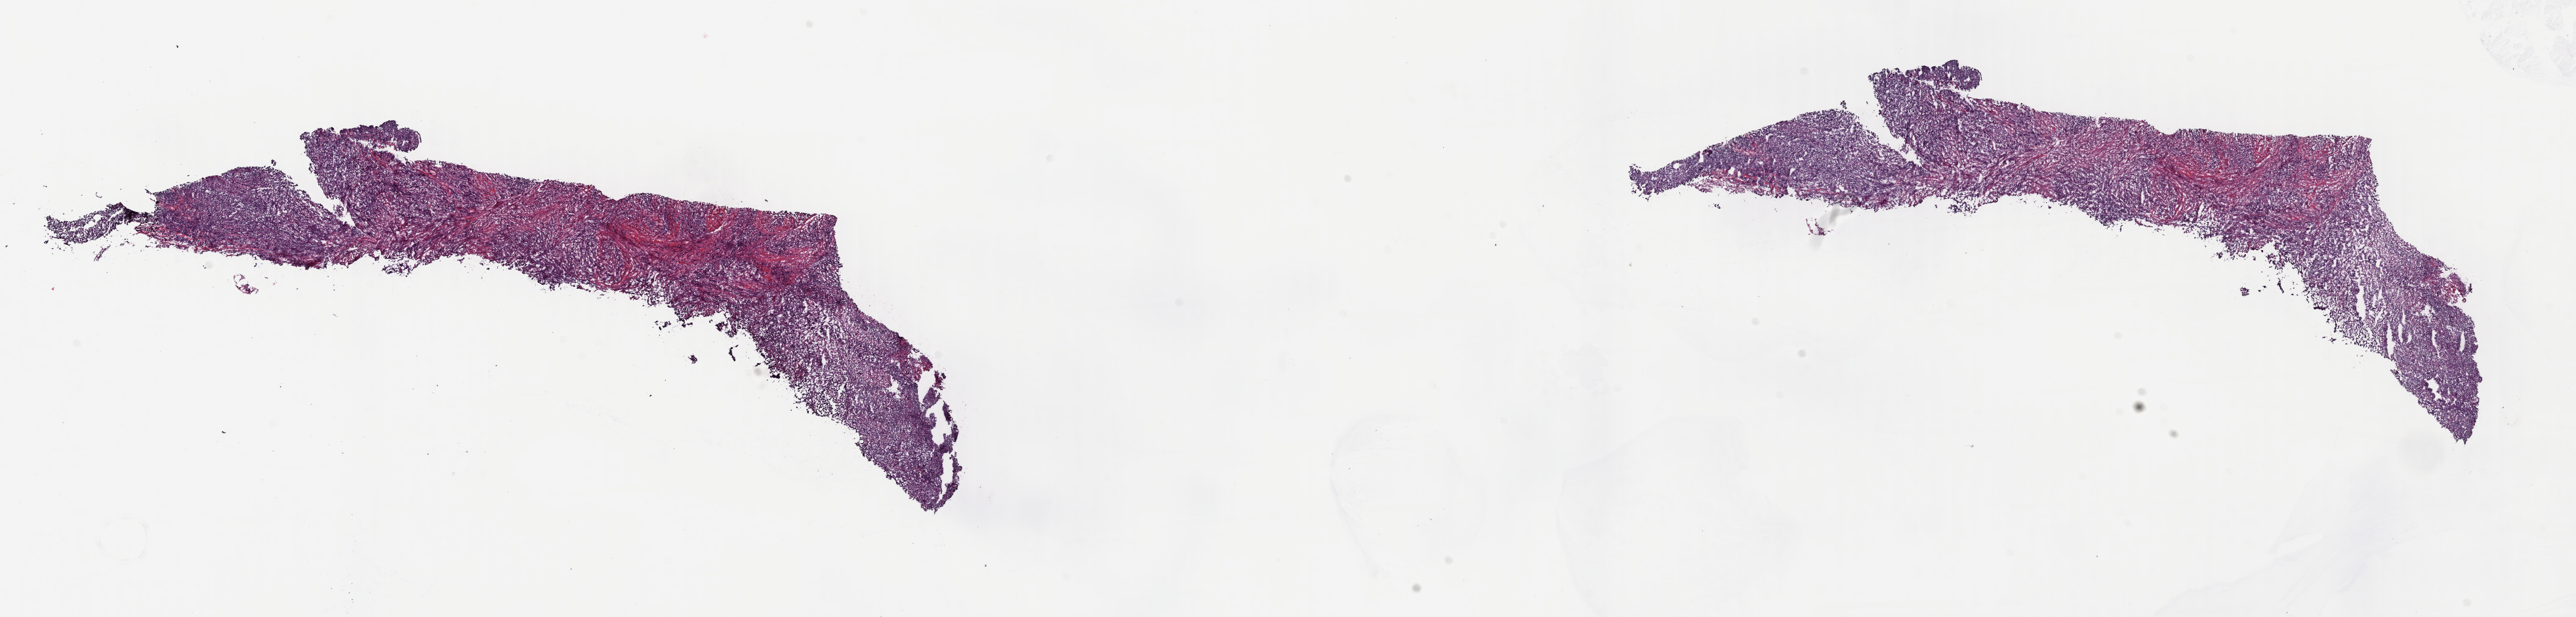
Whole-slide histology image, Hematoxylin and eosin (H&E) stained — low-resolution overview of the scanned area, about 30.9 x 7.4 mm (from a 40x scan); frozen section from the top of the tissue portion; primary tumour sample from the bladder. Male patient; age at initial diagnosis 68 years. Histologic grade: high grade. Composition of this section per pathologist review: tumour cells 70%, tumour nuclei 70%, normal cells 0%, stromal cells 26%, necrosis 4%. Infiltration values recorded for this section: lymphocyte infiltration 6%, monocyte infiltration 3%, neutrophil infiltration 5%.
• AJCC pathologic stage: III (7th edition)
• pathologic diagnosis: Transitional cell carcinoma (posterior wall of bladder)
• lymph nodes positive (case pathology): 0 of 23 examined